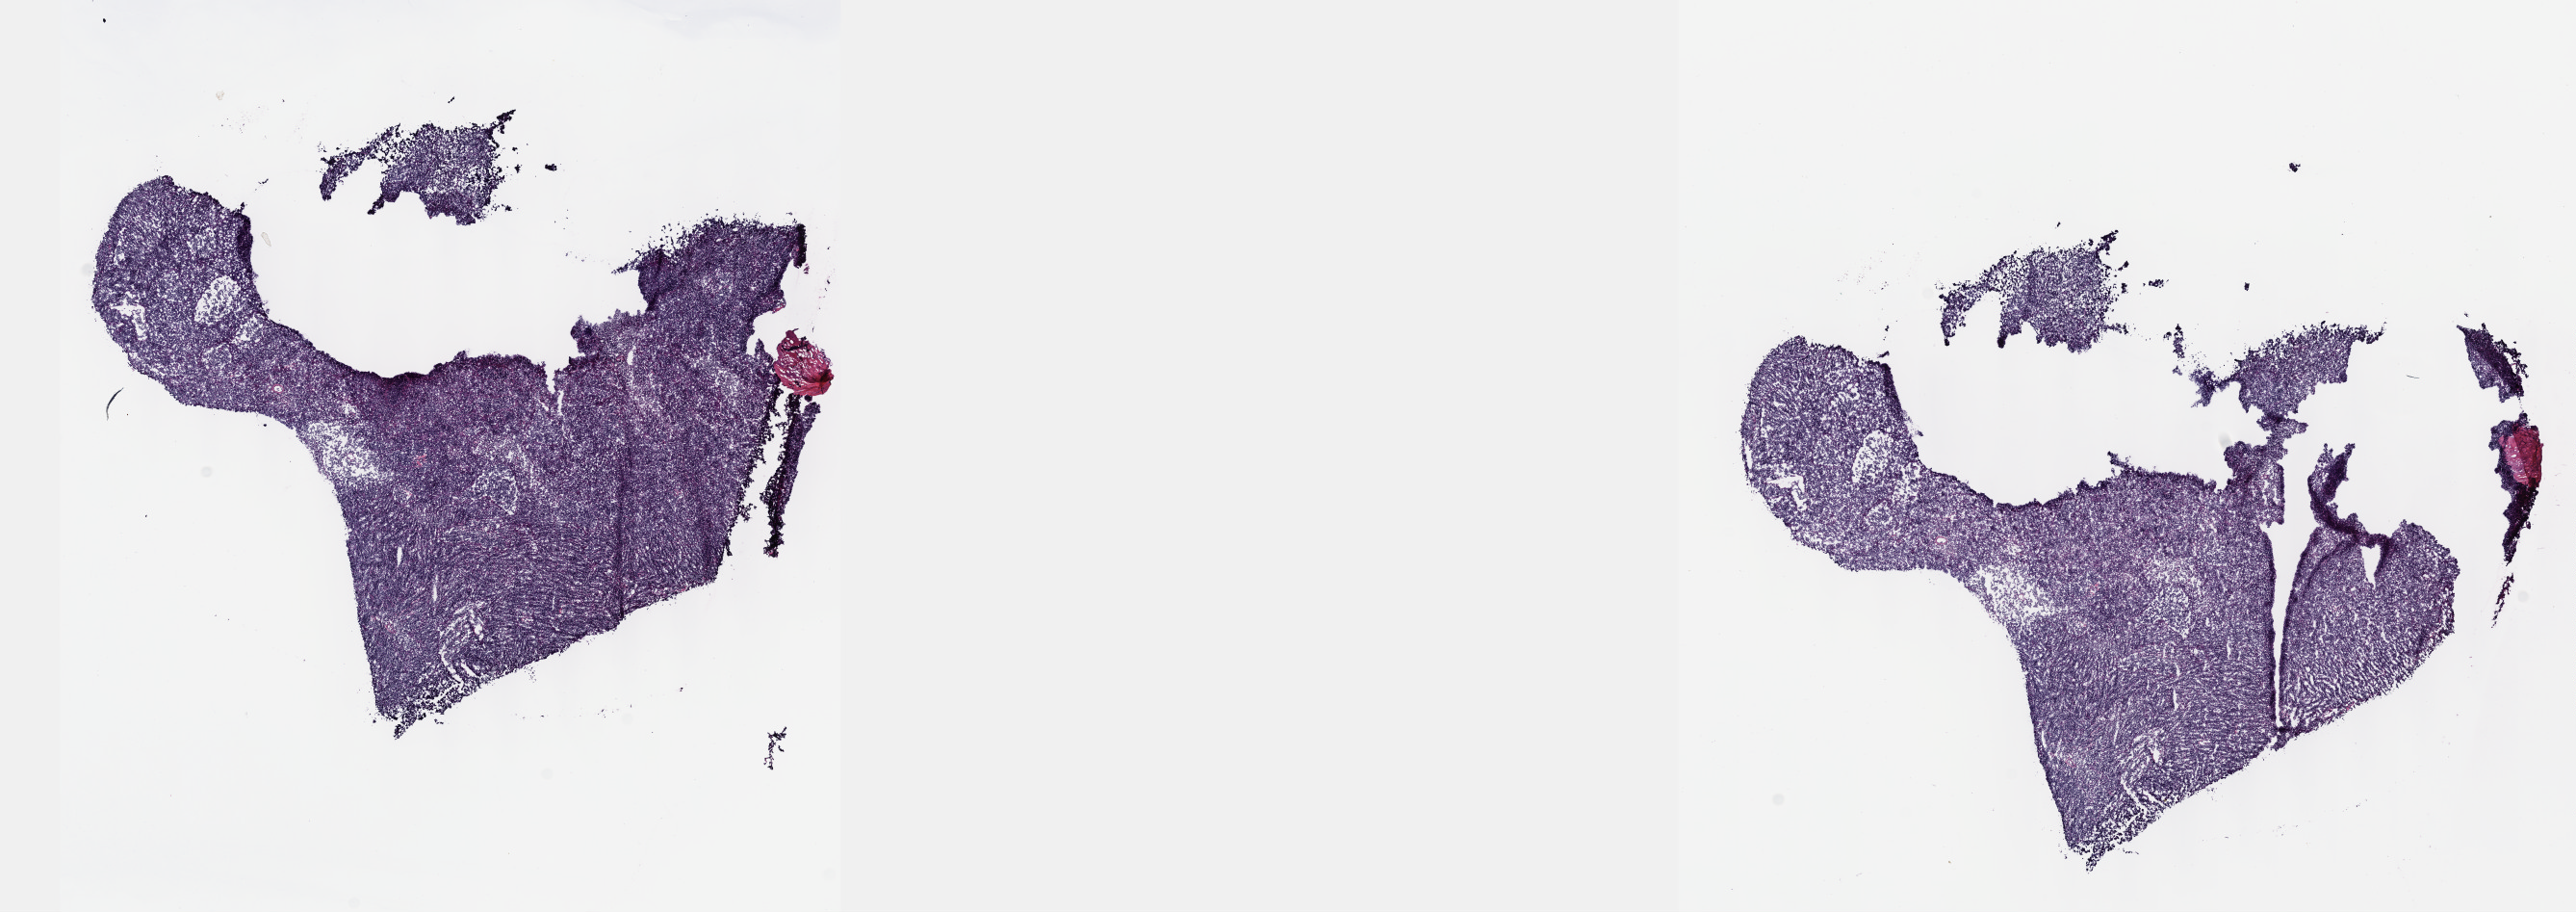
Whole-slide histology image, Hematoxylin and eosin (H&E) stained — whole scanned area (about 21.6 x 7.7 mm, acquisition: 40x scan) shown as a low-resolution overview. Frozen section from the top of the tissue portion. Primary tumour sample from the thymus. Male, age 26 years at initial diagnosis.
Diagnosis: Thymoma, type B2, malignant (anterior mediastinum).